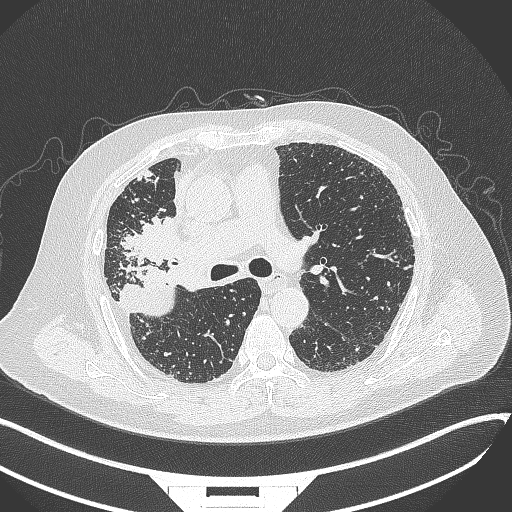
Chest CT, one axial slice. Slice 214 of 384 in the series (ordered by position). 120 kVp. Lung window (W 1500 / L -600 HU). 1 mm slice thickness. 512 × 512 image matrix, field of view 400 × 400 mm. Male patient, age 69 years. Case-level facts recorded for this patient, not image findings: clinical TNM (as recorded): T4 N3 M1.
Outlined on this slice (rectangle marked by the reading radiologist):
- lung tumour (recorded histology: adenocarcinoma): bounding box (x1, y1, x2, y2) in pixels: (119, 210, 194, 270)